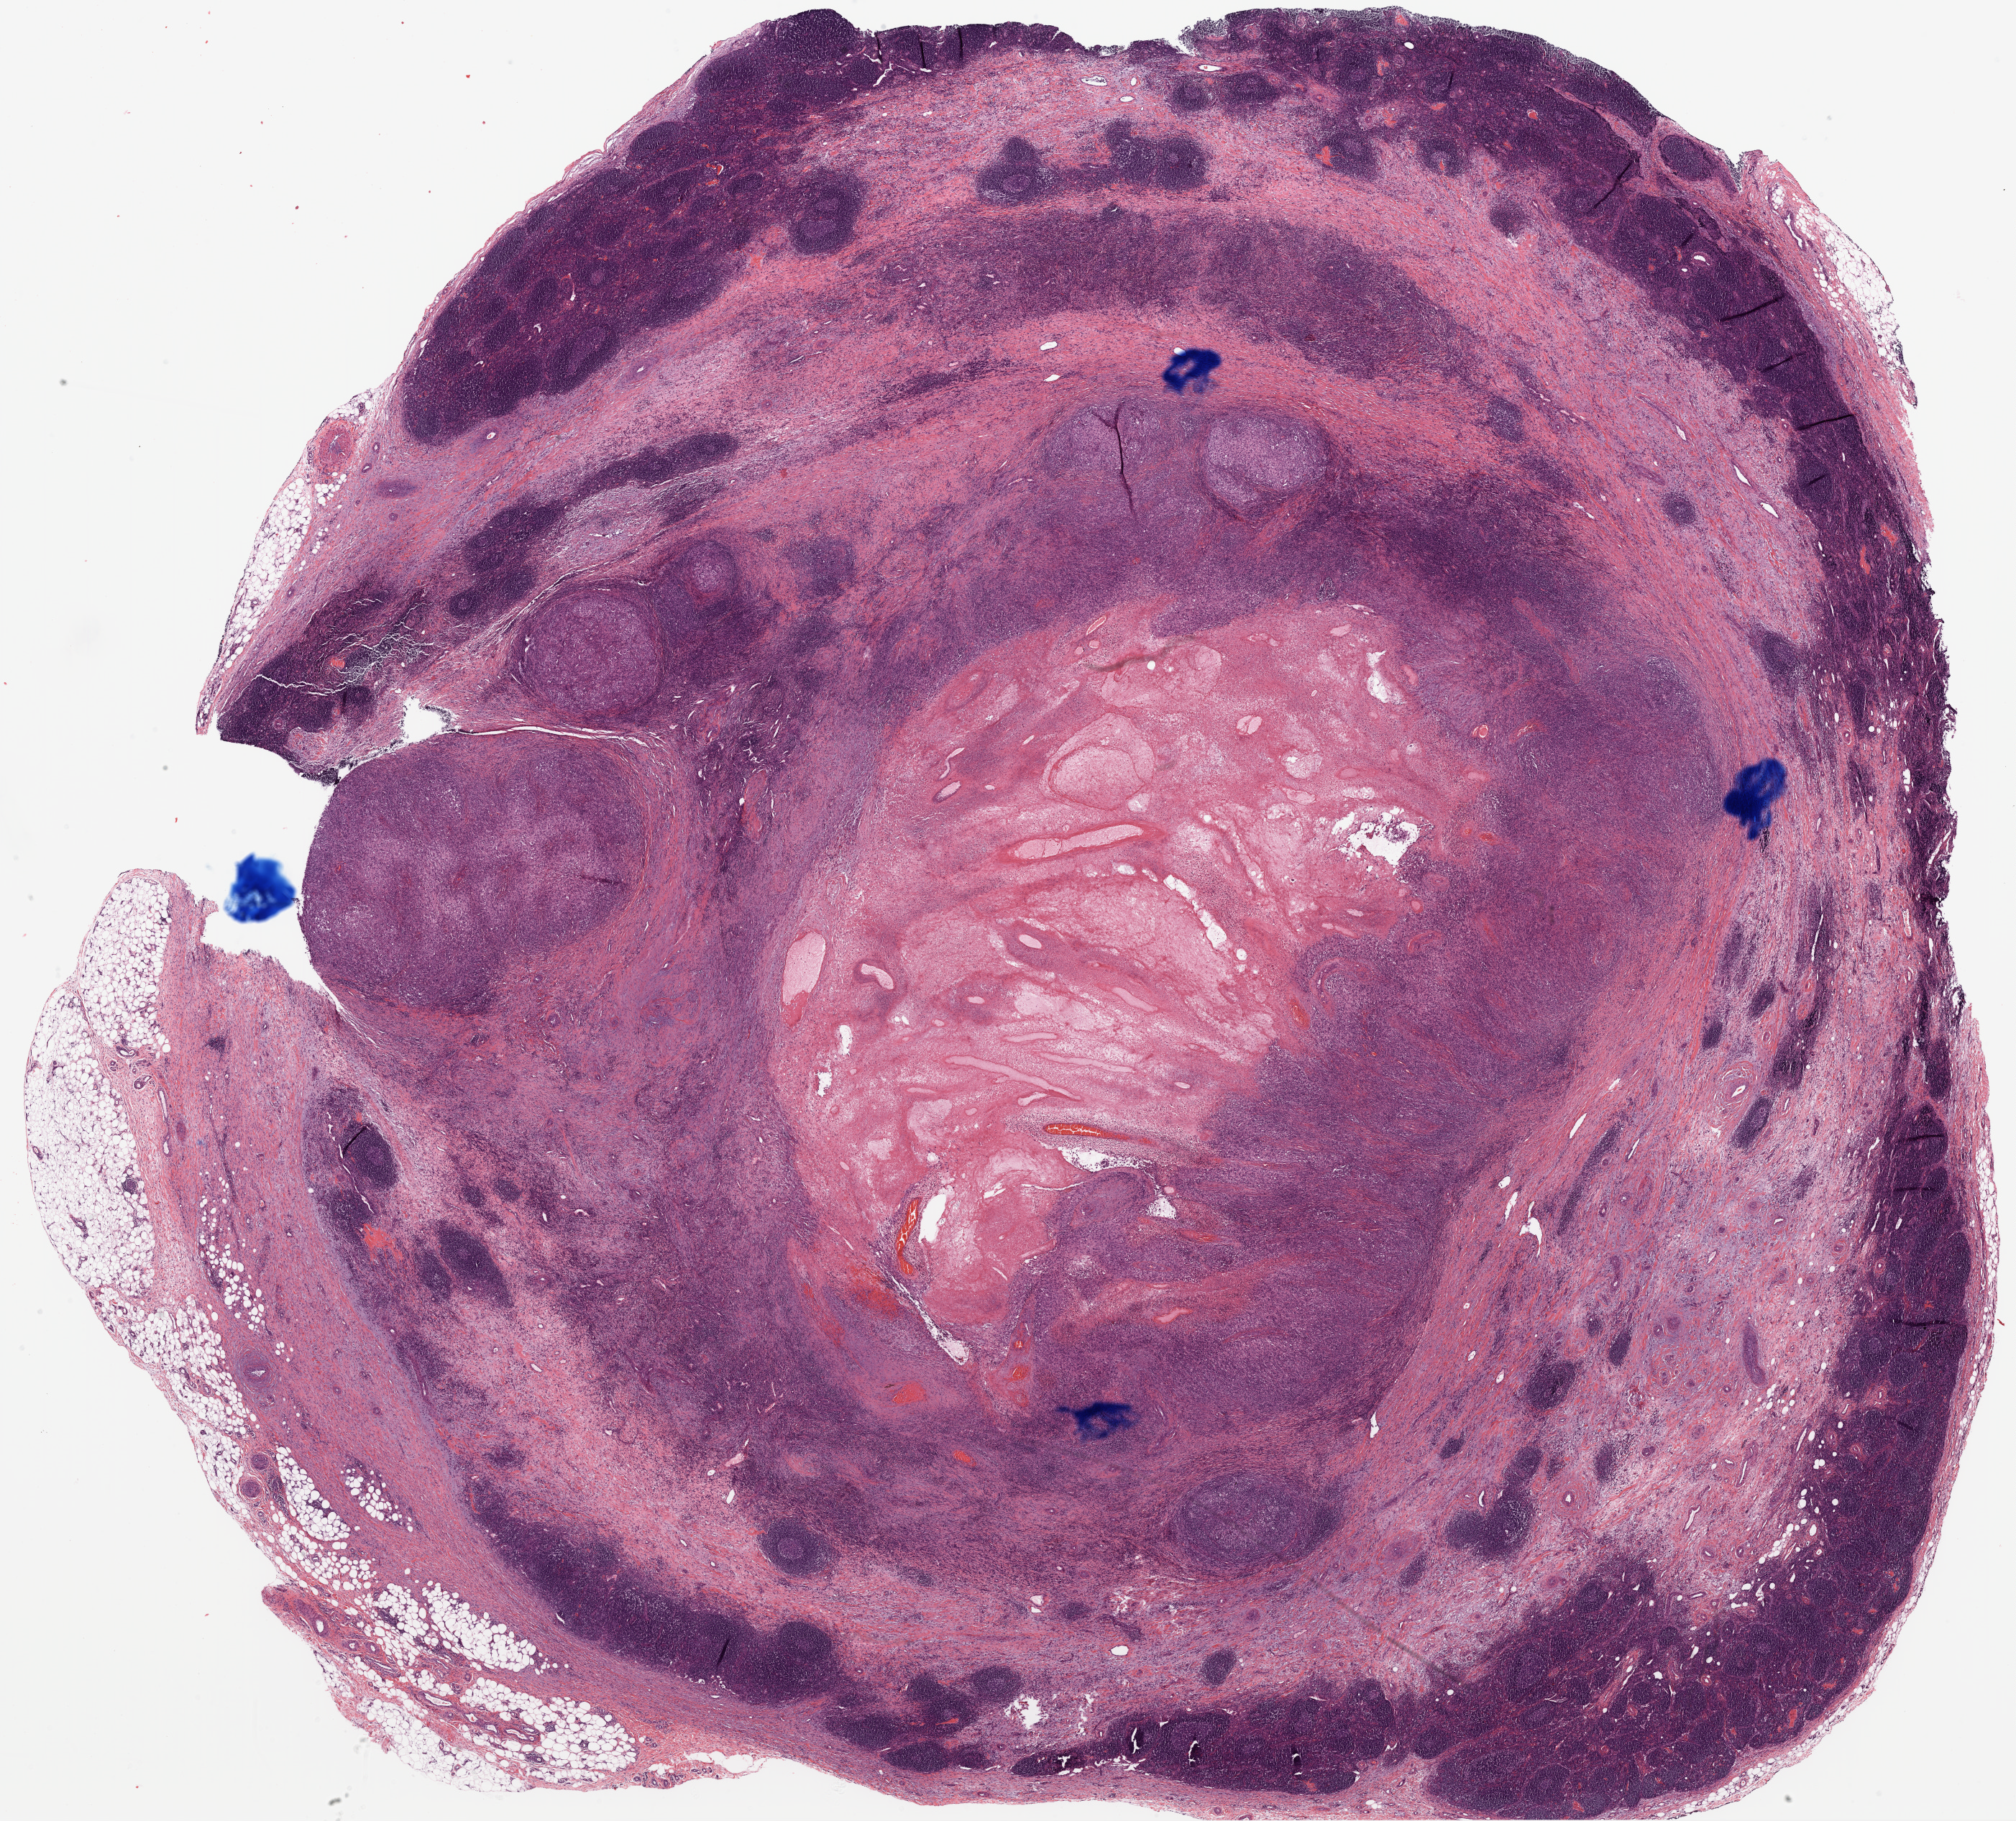
Digitized Hematoxylin and eosin (H&E) stained tissue section (whole slide), a low-resolution overview of the entire scanned area, about 22.6 x 20.4 mm (from a 20x scan). Formalin-fixed paraffin-embedded (FFPE) diagnostic section. Metastatic tumour sample, sampled site: connective, subcutaneous and other soft tissues of lower limb and hip. Patient sex: male.
* this section: metastatic tumour tissue
* patient diagnosis: Malignant melanoma, NOS